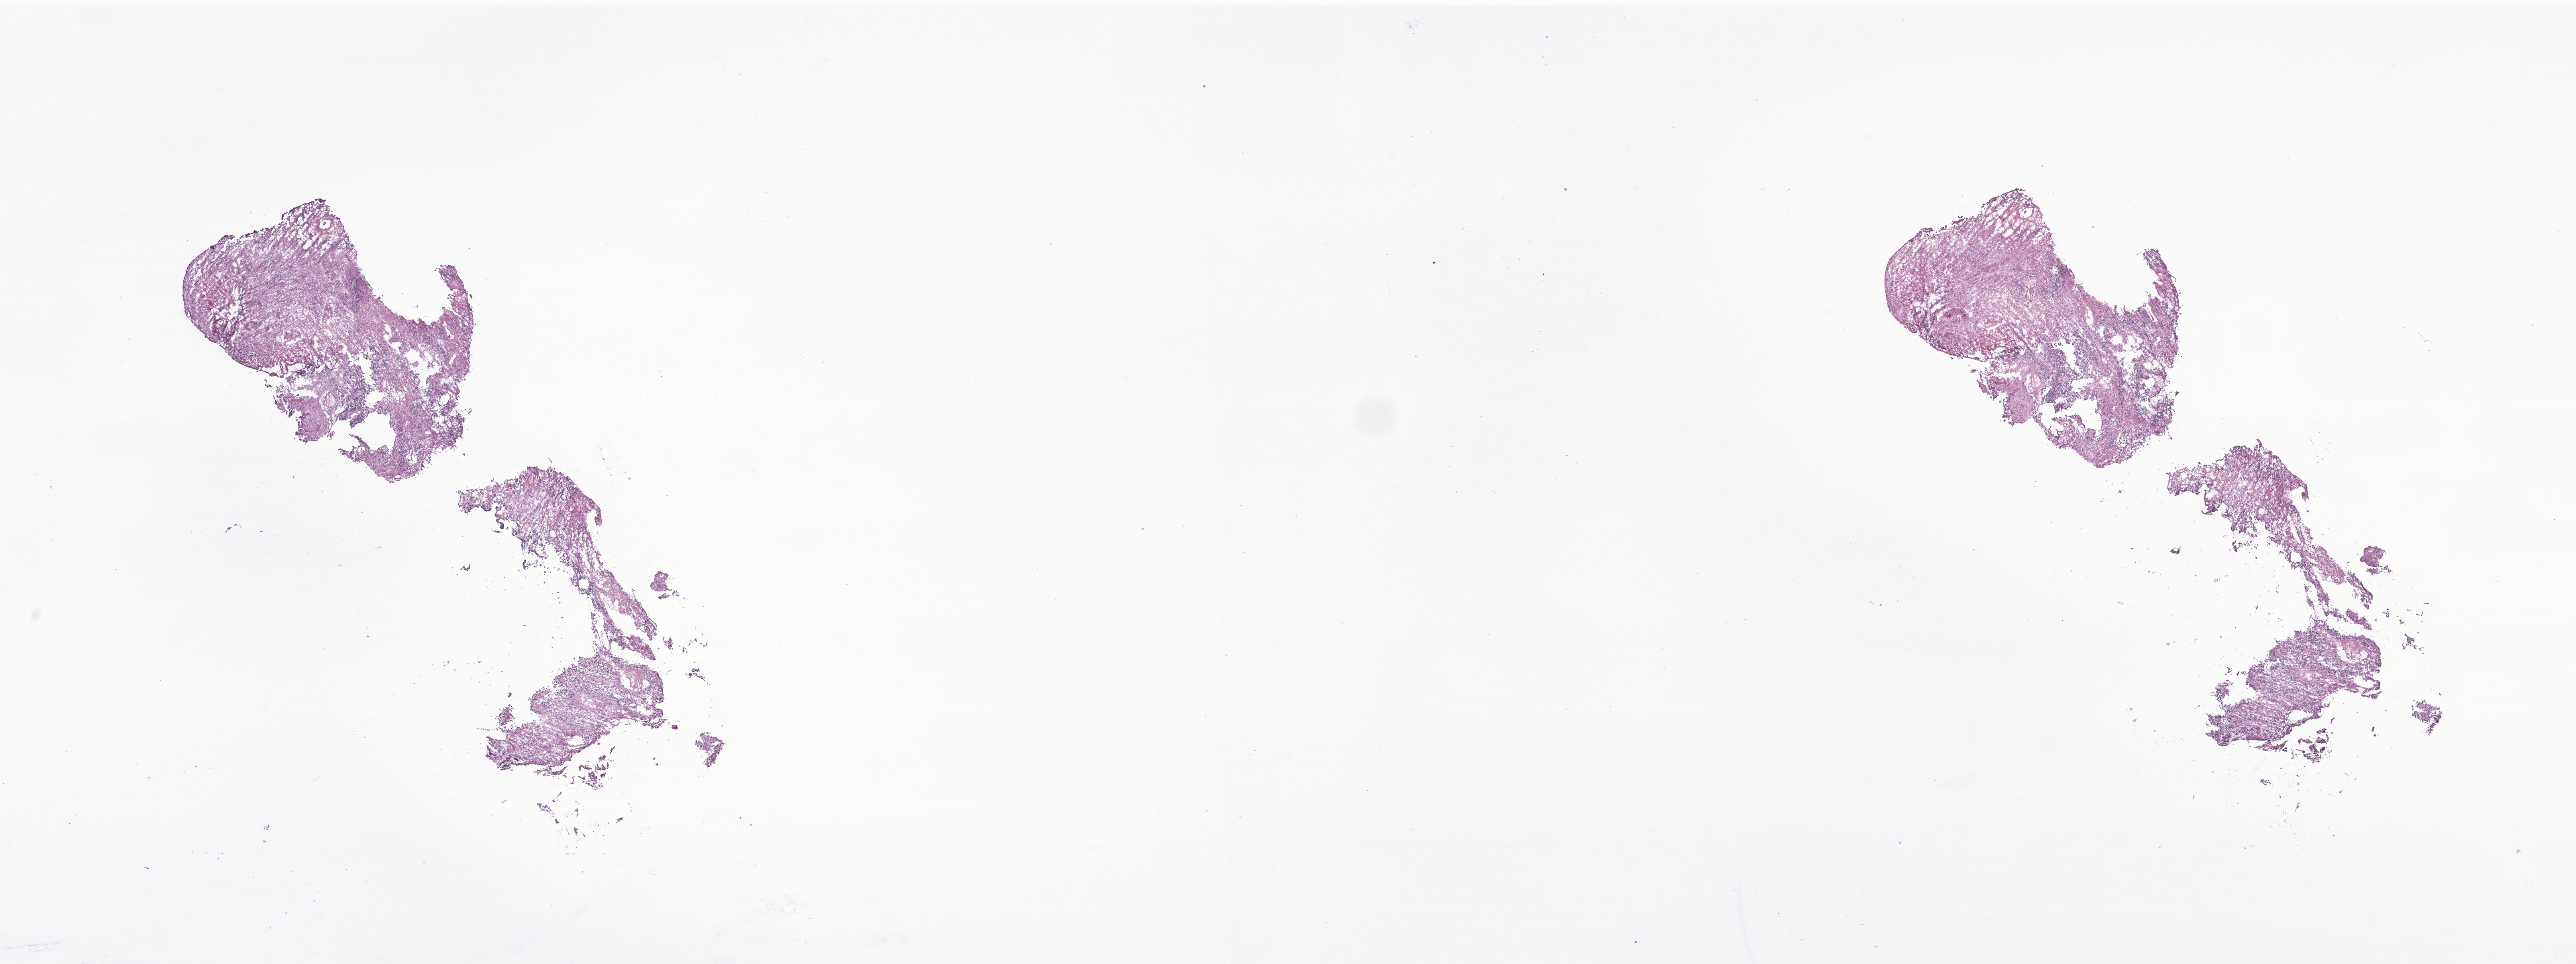
Digitized haematoxylin and eosin-stained section of tumor tissue from the brain, low-resolution overview of the scanned area, about 27.3 x 10.2 mm; frozen section. Patient male; age 898 days.
• diagnosis (ICD-O-3 morphology term): Ependymoma, NOS